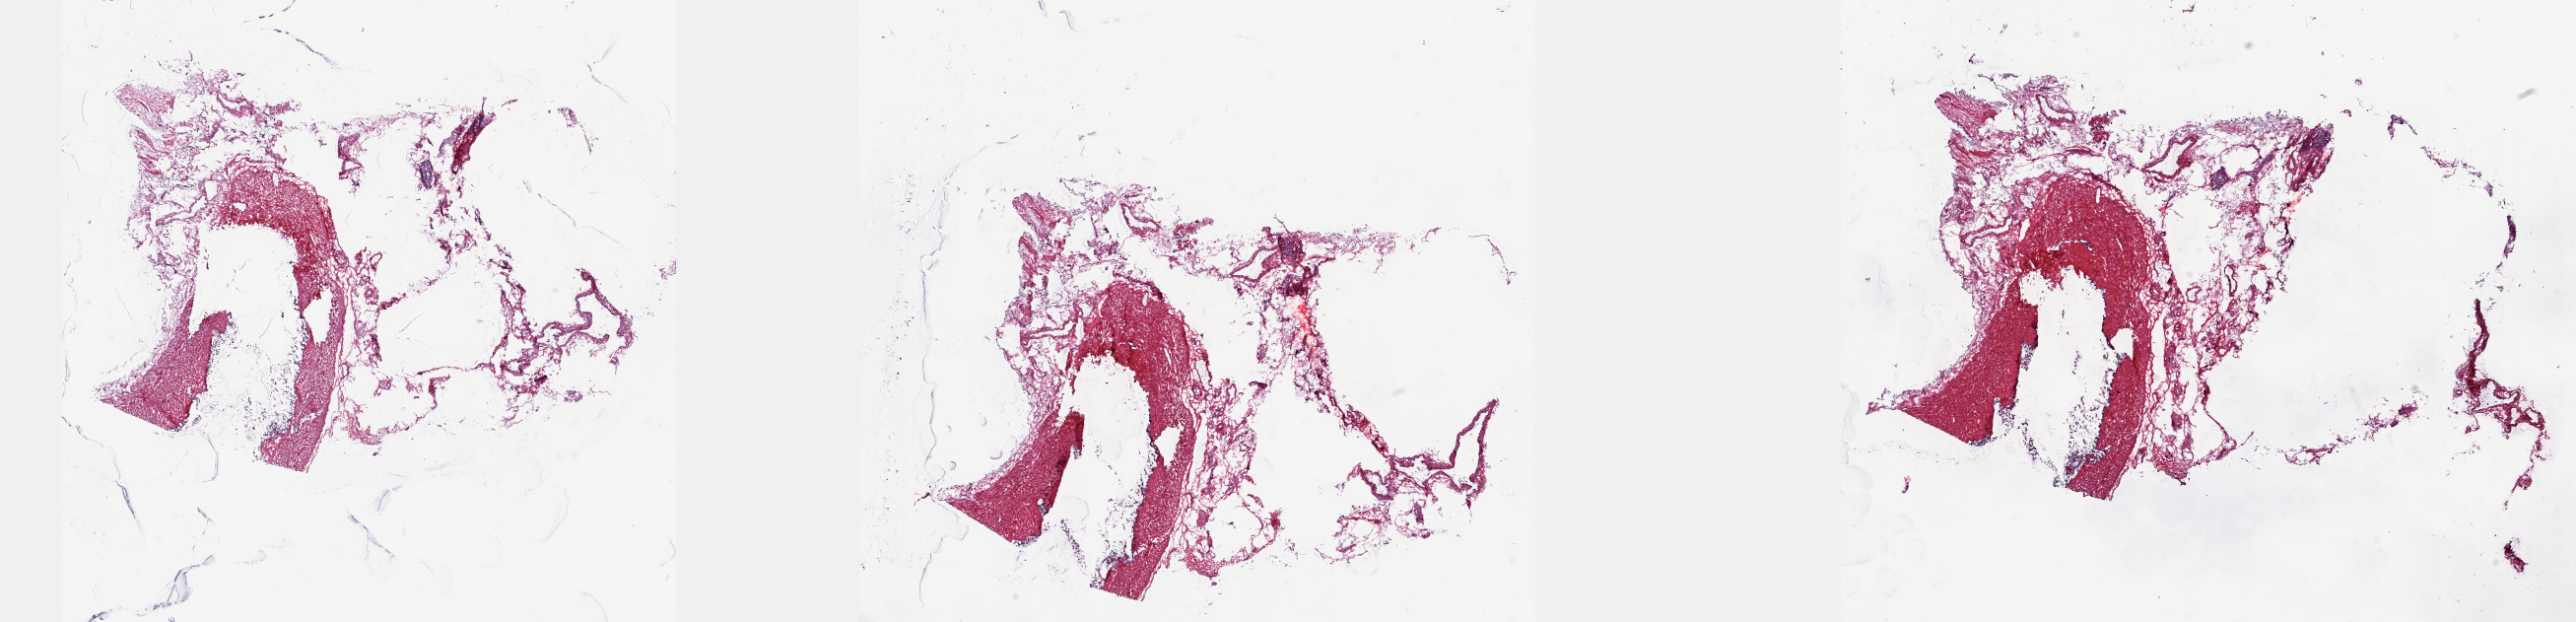
Digitized Hematoxylin and eosin (H&E) stained tissue section (whole slide) — shown as a low-resolution overview of the whole scanned area (about 42.2 x 10.2 mm, acquisition: 20x scan); frozen section from the top of the tissue portion; sample: solid tissue normal (non-tumour tissue), prostate. Male, age 70 years at initial diagnosis. Composition of this section per pathologist review: tumour cells 0%, tumour nuclei 0%, normal cells 100%, stromal cells 0%, necrosis 0%. Infiltration values recorded for this section: lymphocyte infiltration 0%, monocyte infiltration 0%, neutrophil infiltration 0%.
- this section: solid tissue normal sample (biorepository sample class)
- patient diagnosis: Adenocarcinoma, NOS (prostate gland)